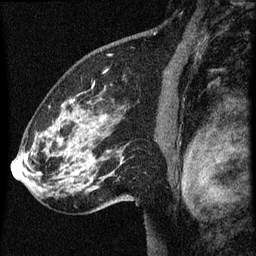
Breast MRI (dynamic contrast-enhanced), one sagittal slice; position 44 of 60 along the scan axis; dynamic contrast-enhanced series, image 2 of 3 at this slice position (ordered by acquisition); 1.5 T; TE 4.2 ms, TR 8 ms; 2 mm slice thickness; 256 × 256 image matrix, field of view 180 × 180 mm. Female patient, age 61 years.
Outlined on this slice (semi-automatically segmented with operator editing):
- analysis volume of interest (the breast-tissue region the enhancement analysis was run in; not a lesion): bounding box [x1, y1, x2, y2] px = [27, 82, 134, 209]
- tumour enhancement mask (voxels above the 70 % enhancement threshold inside the analysis volume of interest): [31, 84, 94, 155]